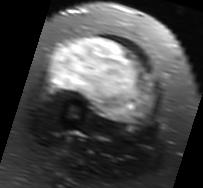
MRI of an extremity soft-tissue mass, one axial slice; position 31 of 91 along the scan axis; T2-weighted fat-saturated; MR volume resampled by the dataset authors to the PET/CT grid (not the native acquisition matrix); 203 × 188 image matrix, field of view 198 × 184 mm. Female patient. Case-level facts recorded for this patient, not image findings: histological type: malignant solitary fibrous tumor; grade: intermediate; site of the primary tumour: right thigh.
Annotated regions visible in this slice (expert contour drawn on MRI and transferred to this co-registered scan by the dataset authors):
- gross tumour volume including surrounding oedema: bounding box <47,37,157,125> (left, top, right, bottom; pixels)
- gross tumour volume (mass): <53,37,153,121>